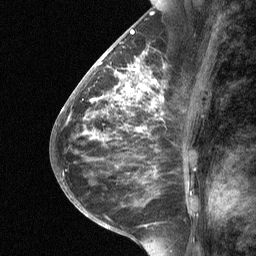
Breast MRI (dynamic contrast-enhanced), one sagittal slice; slice 31 of 64 in the series (ordered by position); dynamic contrast-enhanced study with each time point stored as its own series, time point 2 of 3 at this slice position (early post-contrast, ordered by acquisition time); 1.5 T; TE 4.8 ms, TR 27 ms; 2 mm slice thickness; 256 × 256 image matrix, field of view 180 × 180 mm. Patient: female, 59 years. Case-level facts recorded for this patient, not image findings: setting: breast cancer imaged before/during neoadjuvant chemotherapy; receptor status: triple-negative.
Structures marked on this image (semi-automatic segmentation, software-assisted and operator-edited):
- analysis volume of interest (the breast-tissue region the enhancement analysis was run in; not a lesion): bounding box <113,66,165,119> (left, top, right, bottom; pixels)
- tumour enhancement mask (voxels above the 90 % enhancement threshold inside the analysis volume of interest): <116,66,157,100>